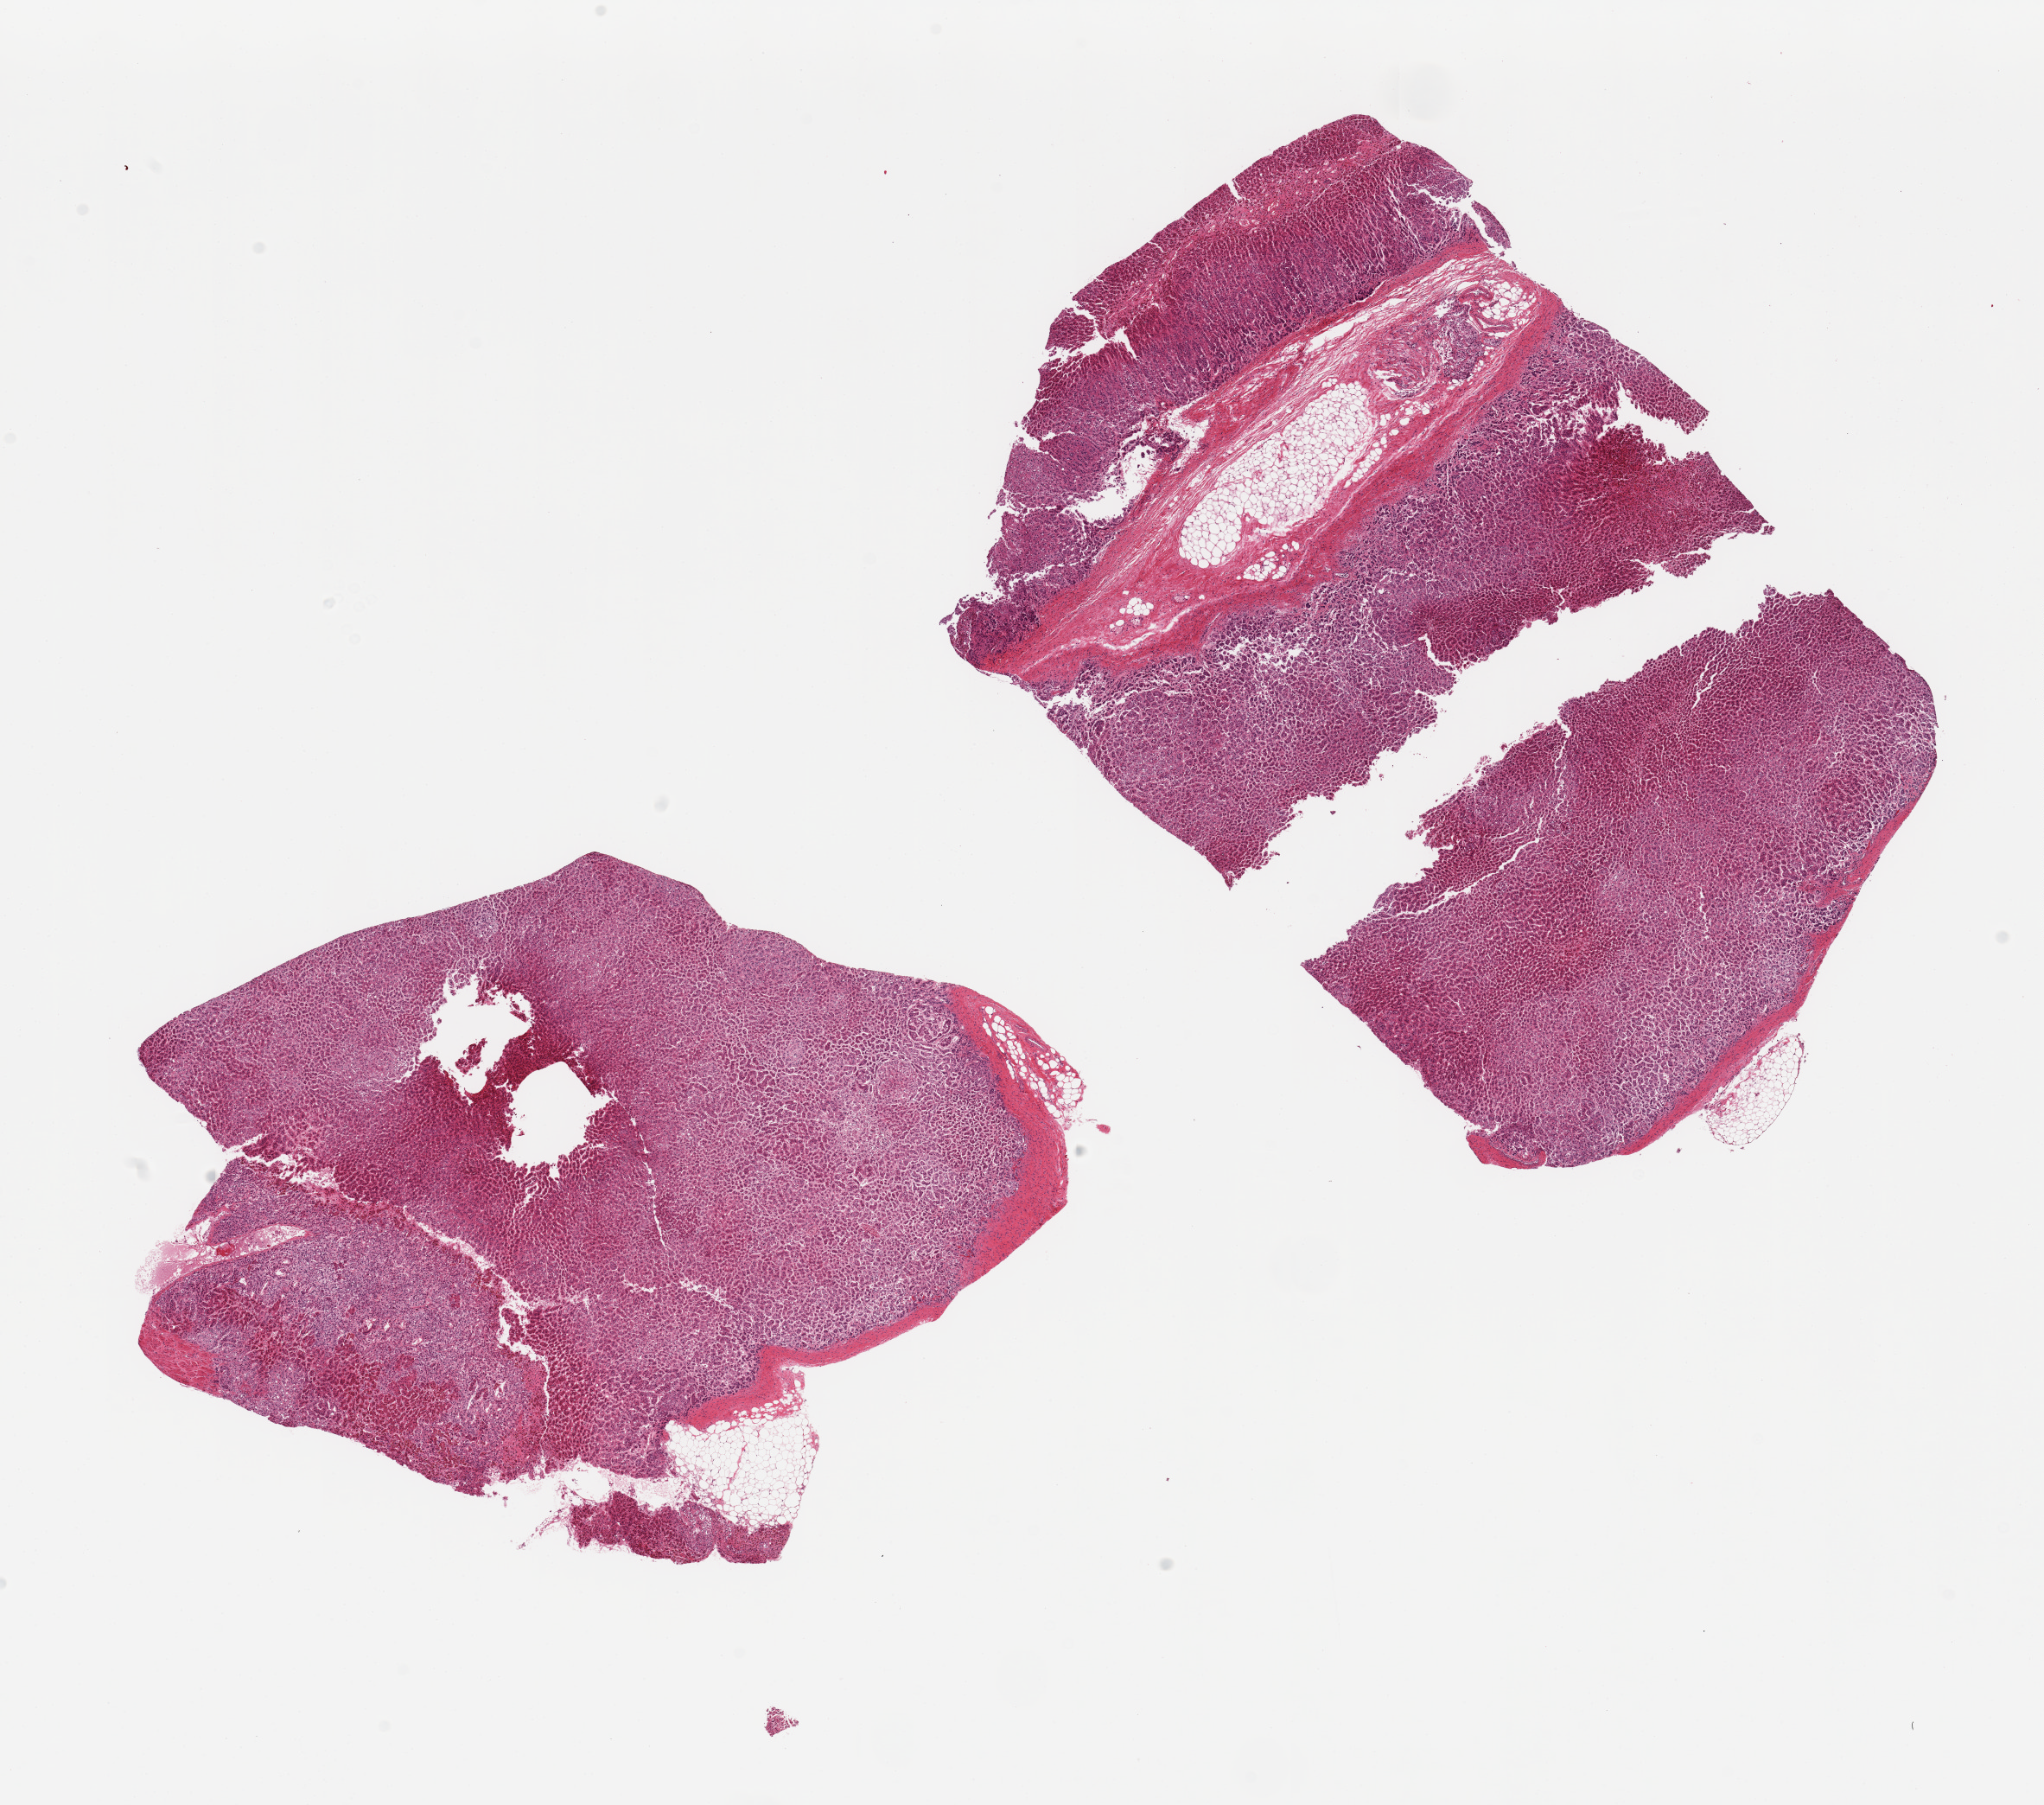
Haematoxylin and eosin whole-slide image, a low-resolution overview of the entire scanned area, about 18.7 x 16.5 mm; PAXgene-fixed, paraffin-embedded tissue; sampled site (target tissue): adrenal gland; donor tissue sample. Male donor.
Pathologist's review note for this sample: 3 pieces; each with small portion of fat (<10%).